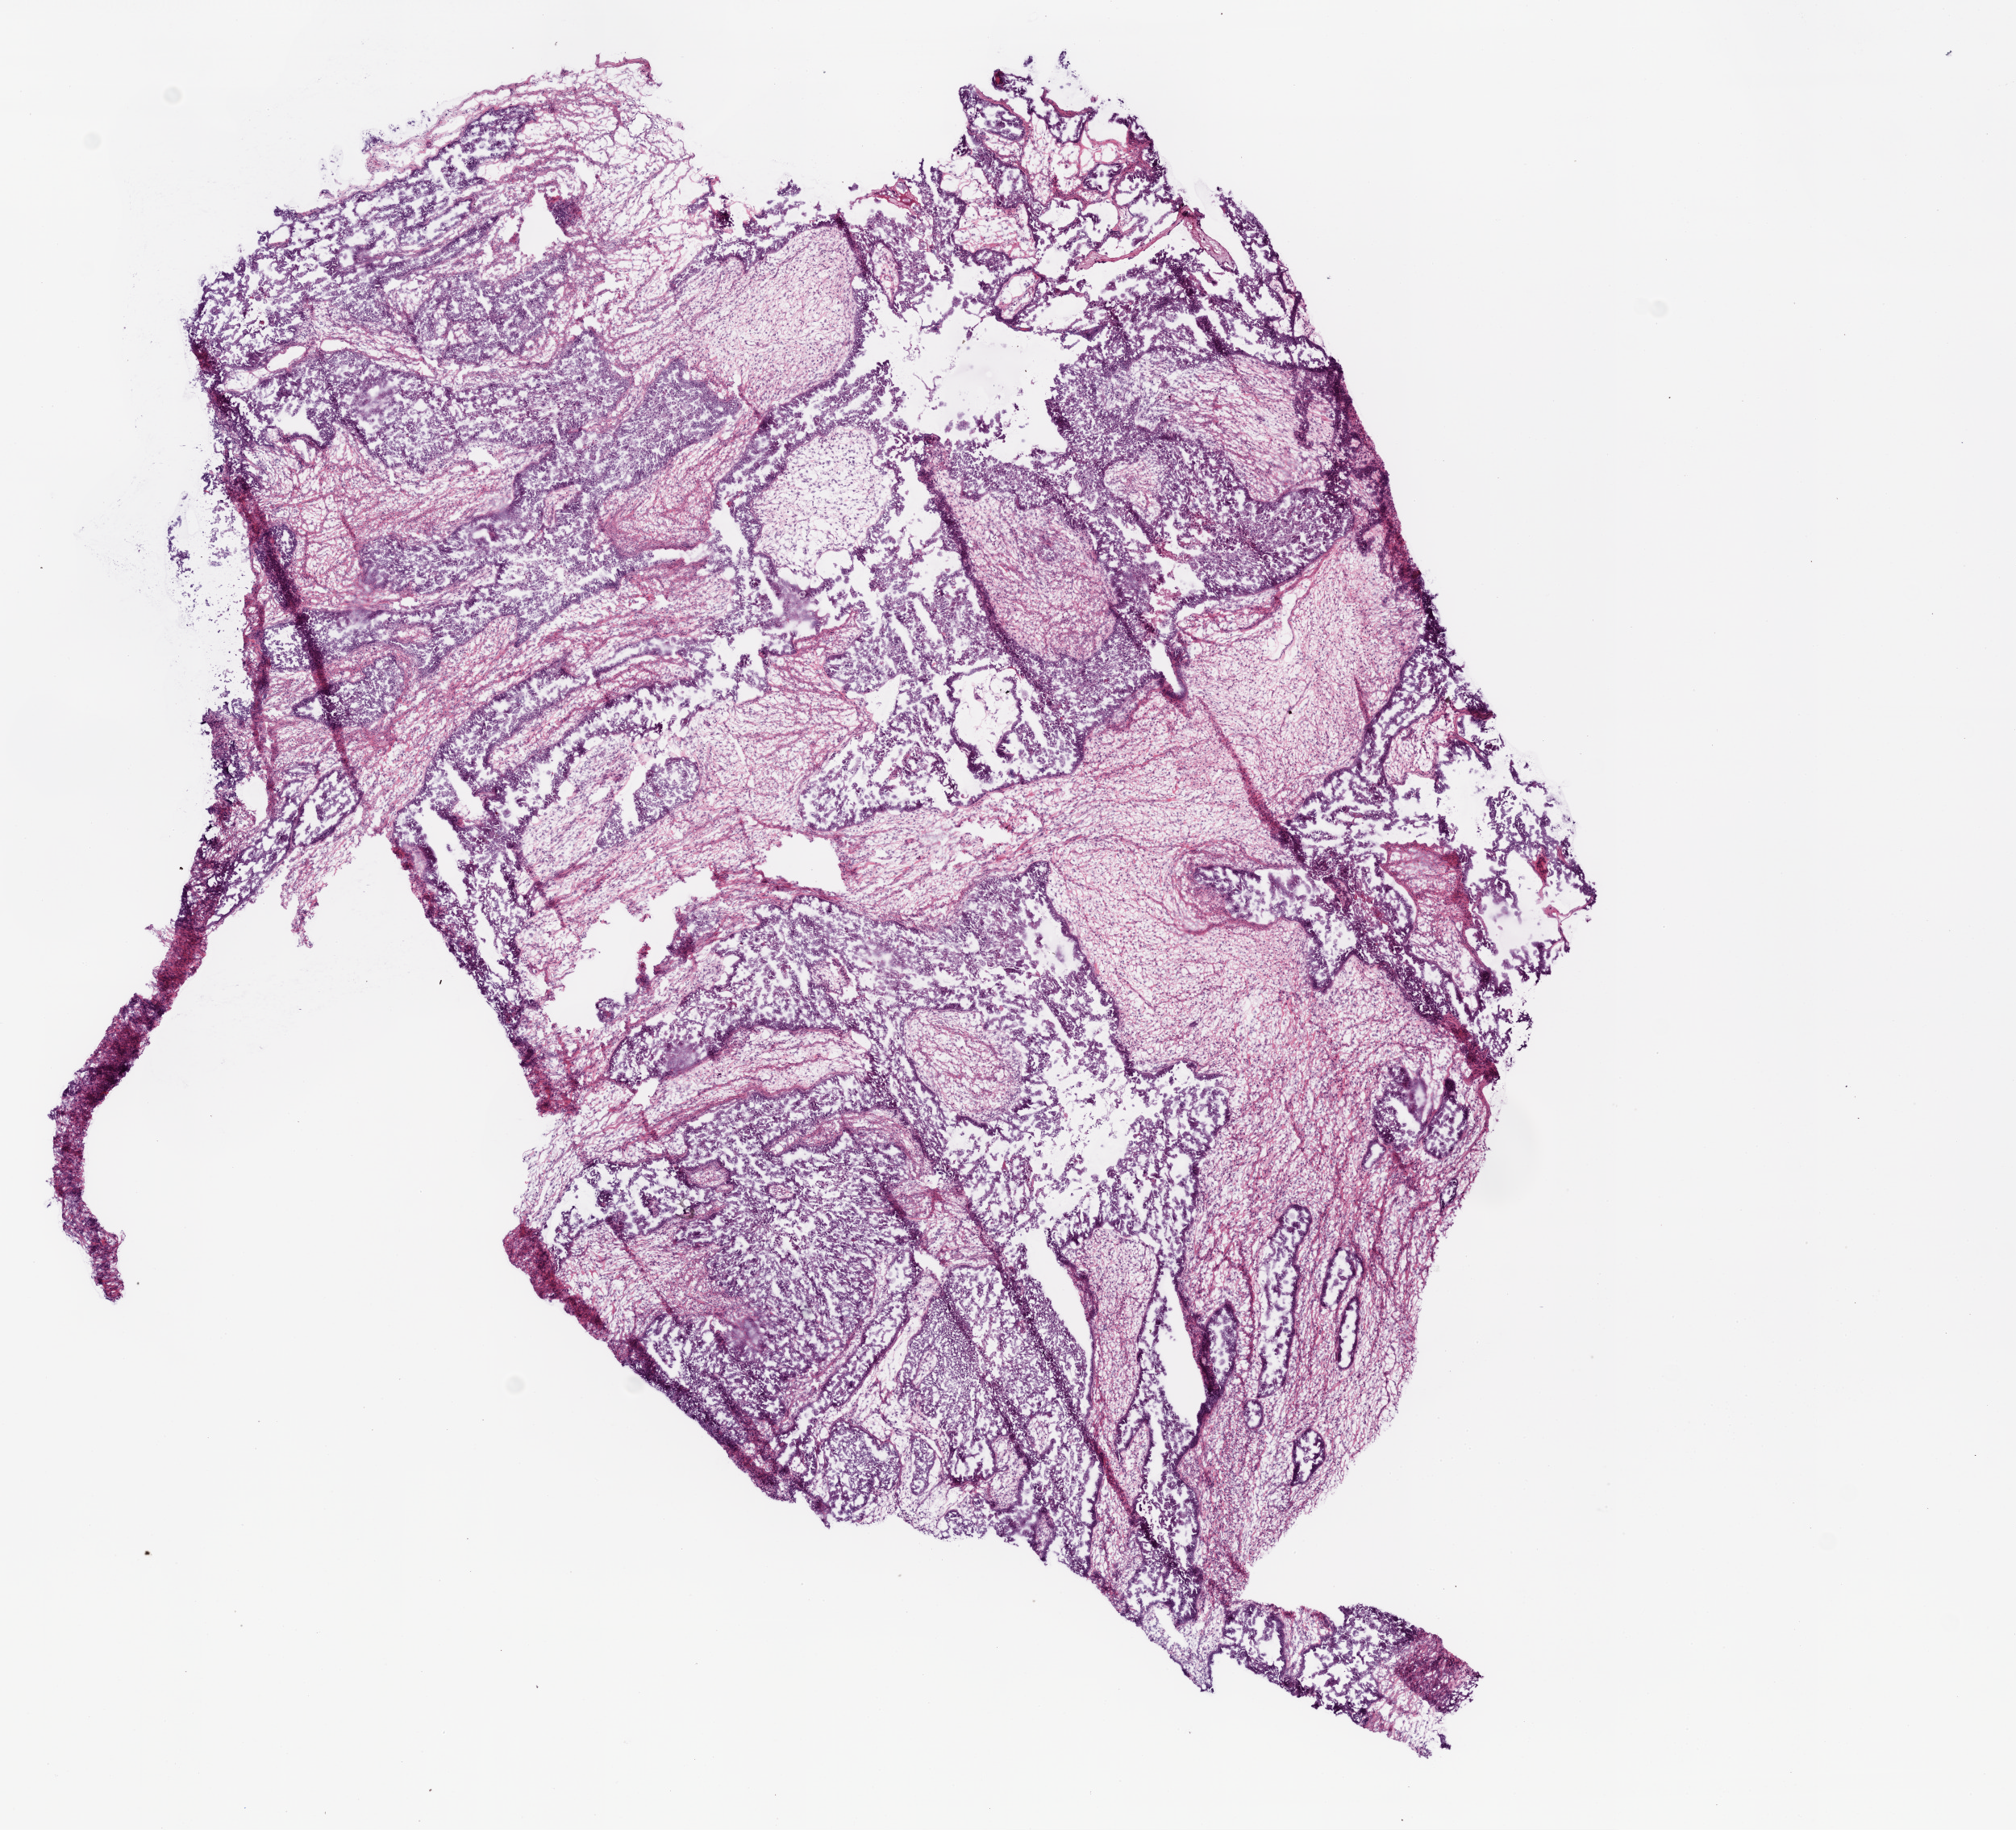
Whole-slide histology image, Hematoxylin and eosin (H&E) stained — low-resolution overview of the scanned area, about 10.0 x 9.1 mm. Frozen section. Ovary, primary tumour sample. Female, age 46 years at initial diagnosis. Histologic grade: G3 (poorly differentiated). Slide review estimates, as recorded: tumour cells 80%, tumour nuclei 80%, normal cells 0%, stromal cells 20%, necrosis 0%.
FIGO stage: IIIC. Laterality: right. Histologic diagnosis: Serous cystadenocarcinoma, NOS.